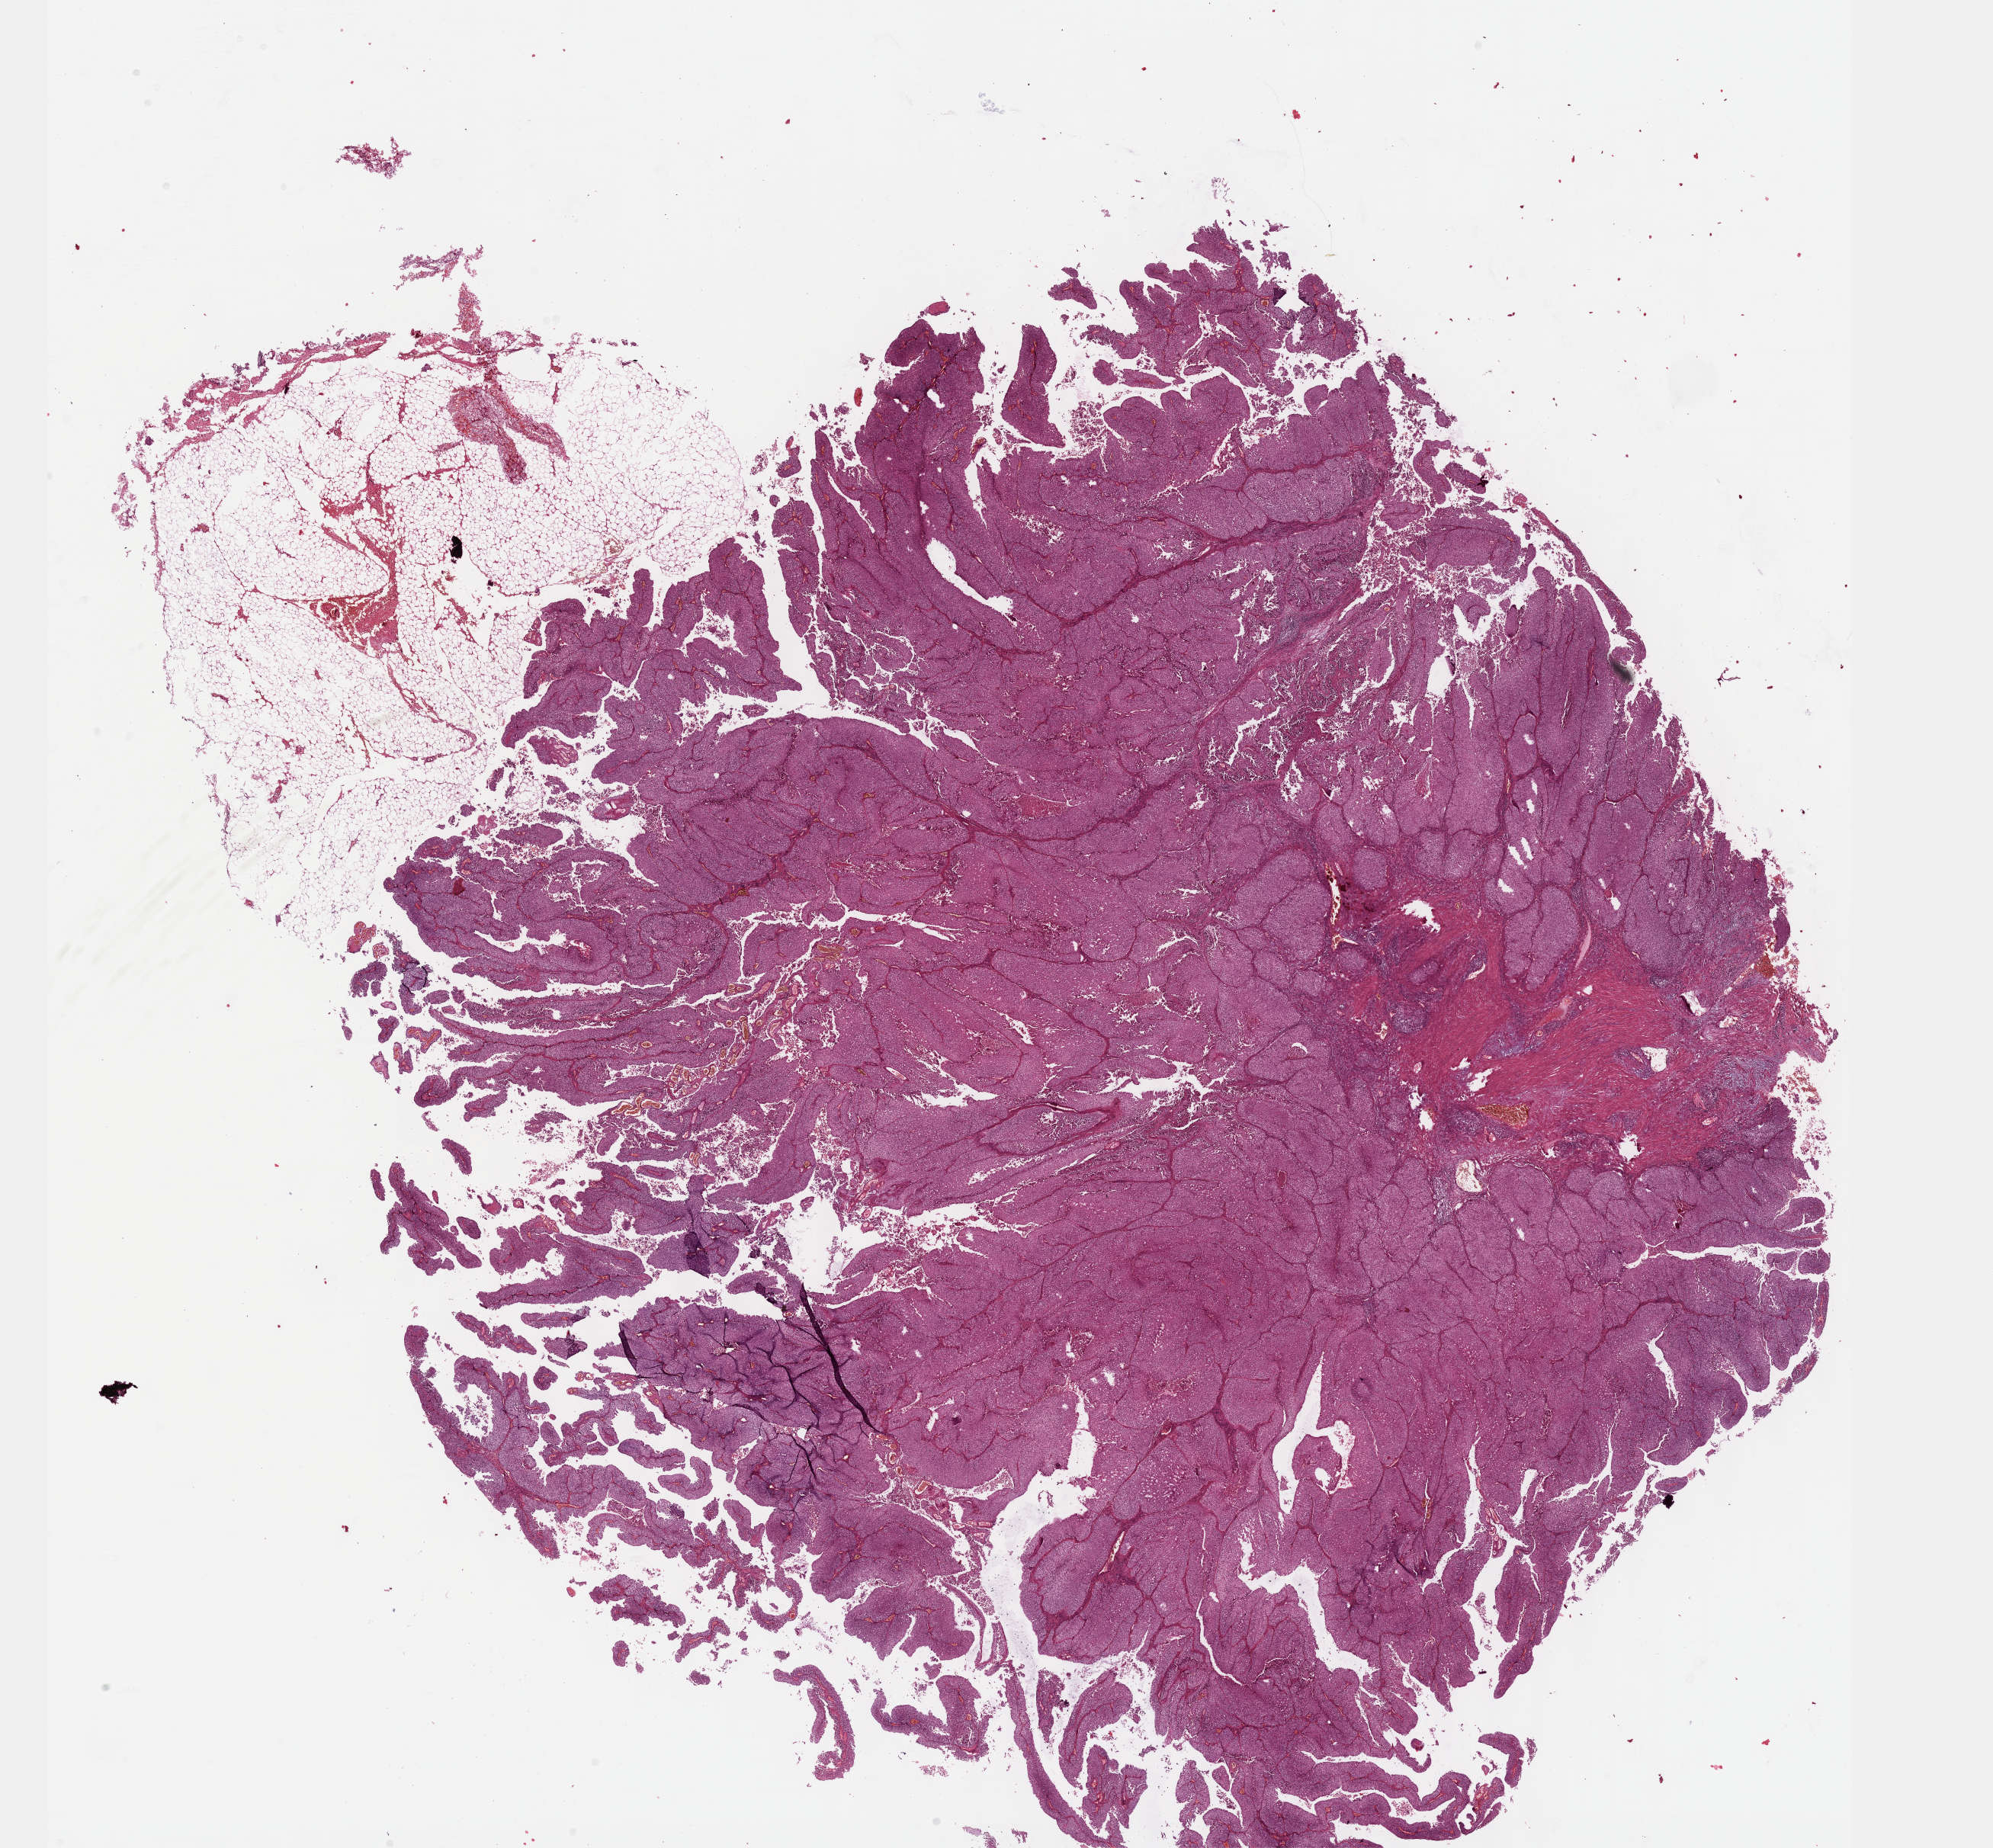
Hematoxylin and eosin (H&E) stained whole-slide image, a low-resolution overview of the entire scanned area, about 21.1 x 19.6 mm (slide scanned at 40x). FFPE section. Kidney, primary tumour sample. Male, age 75 years at initial diagnosis.
Diagnosis: Papillary adenocarcinoma, NOS.